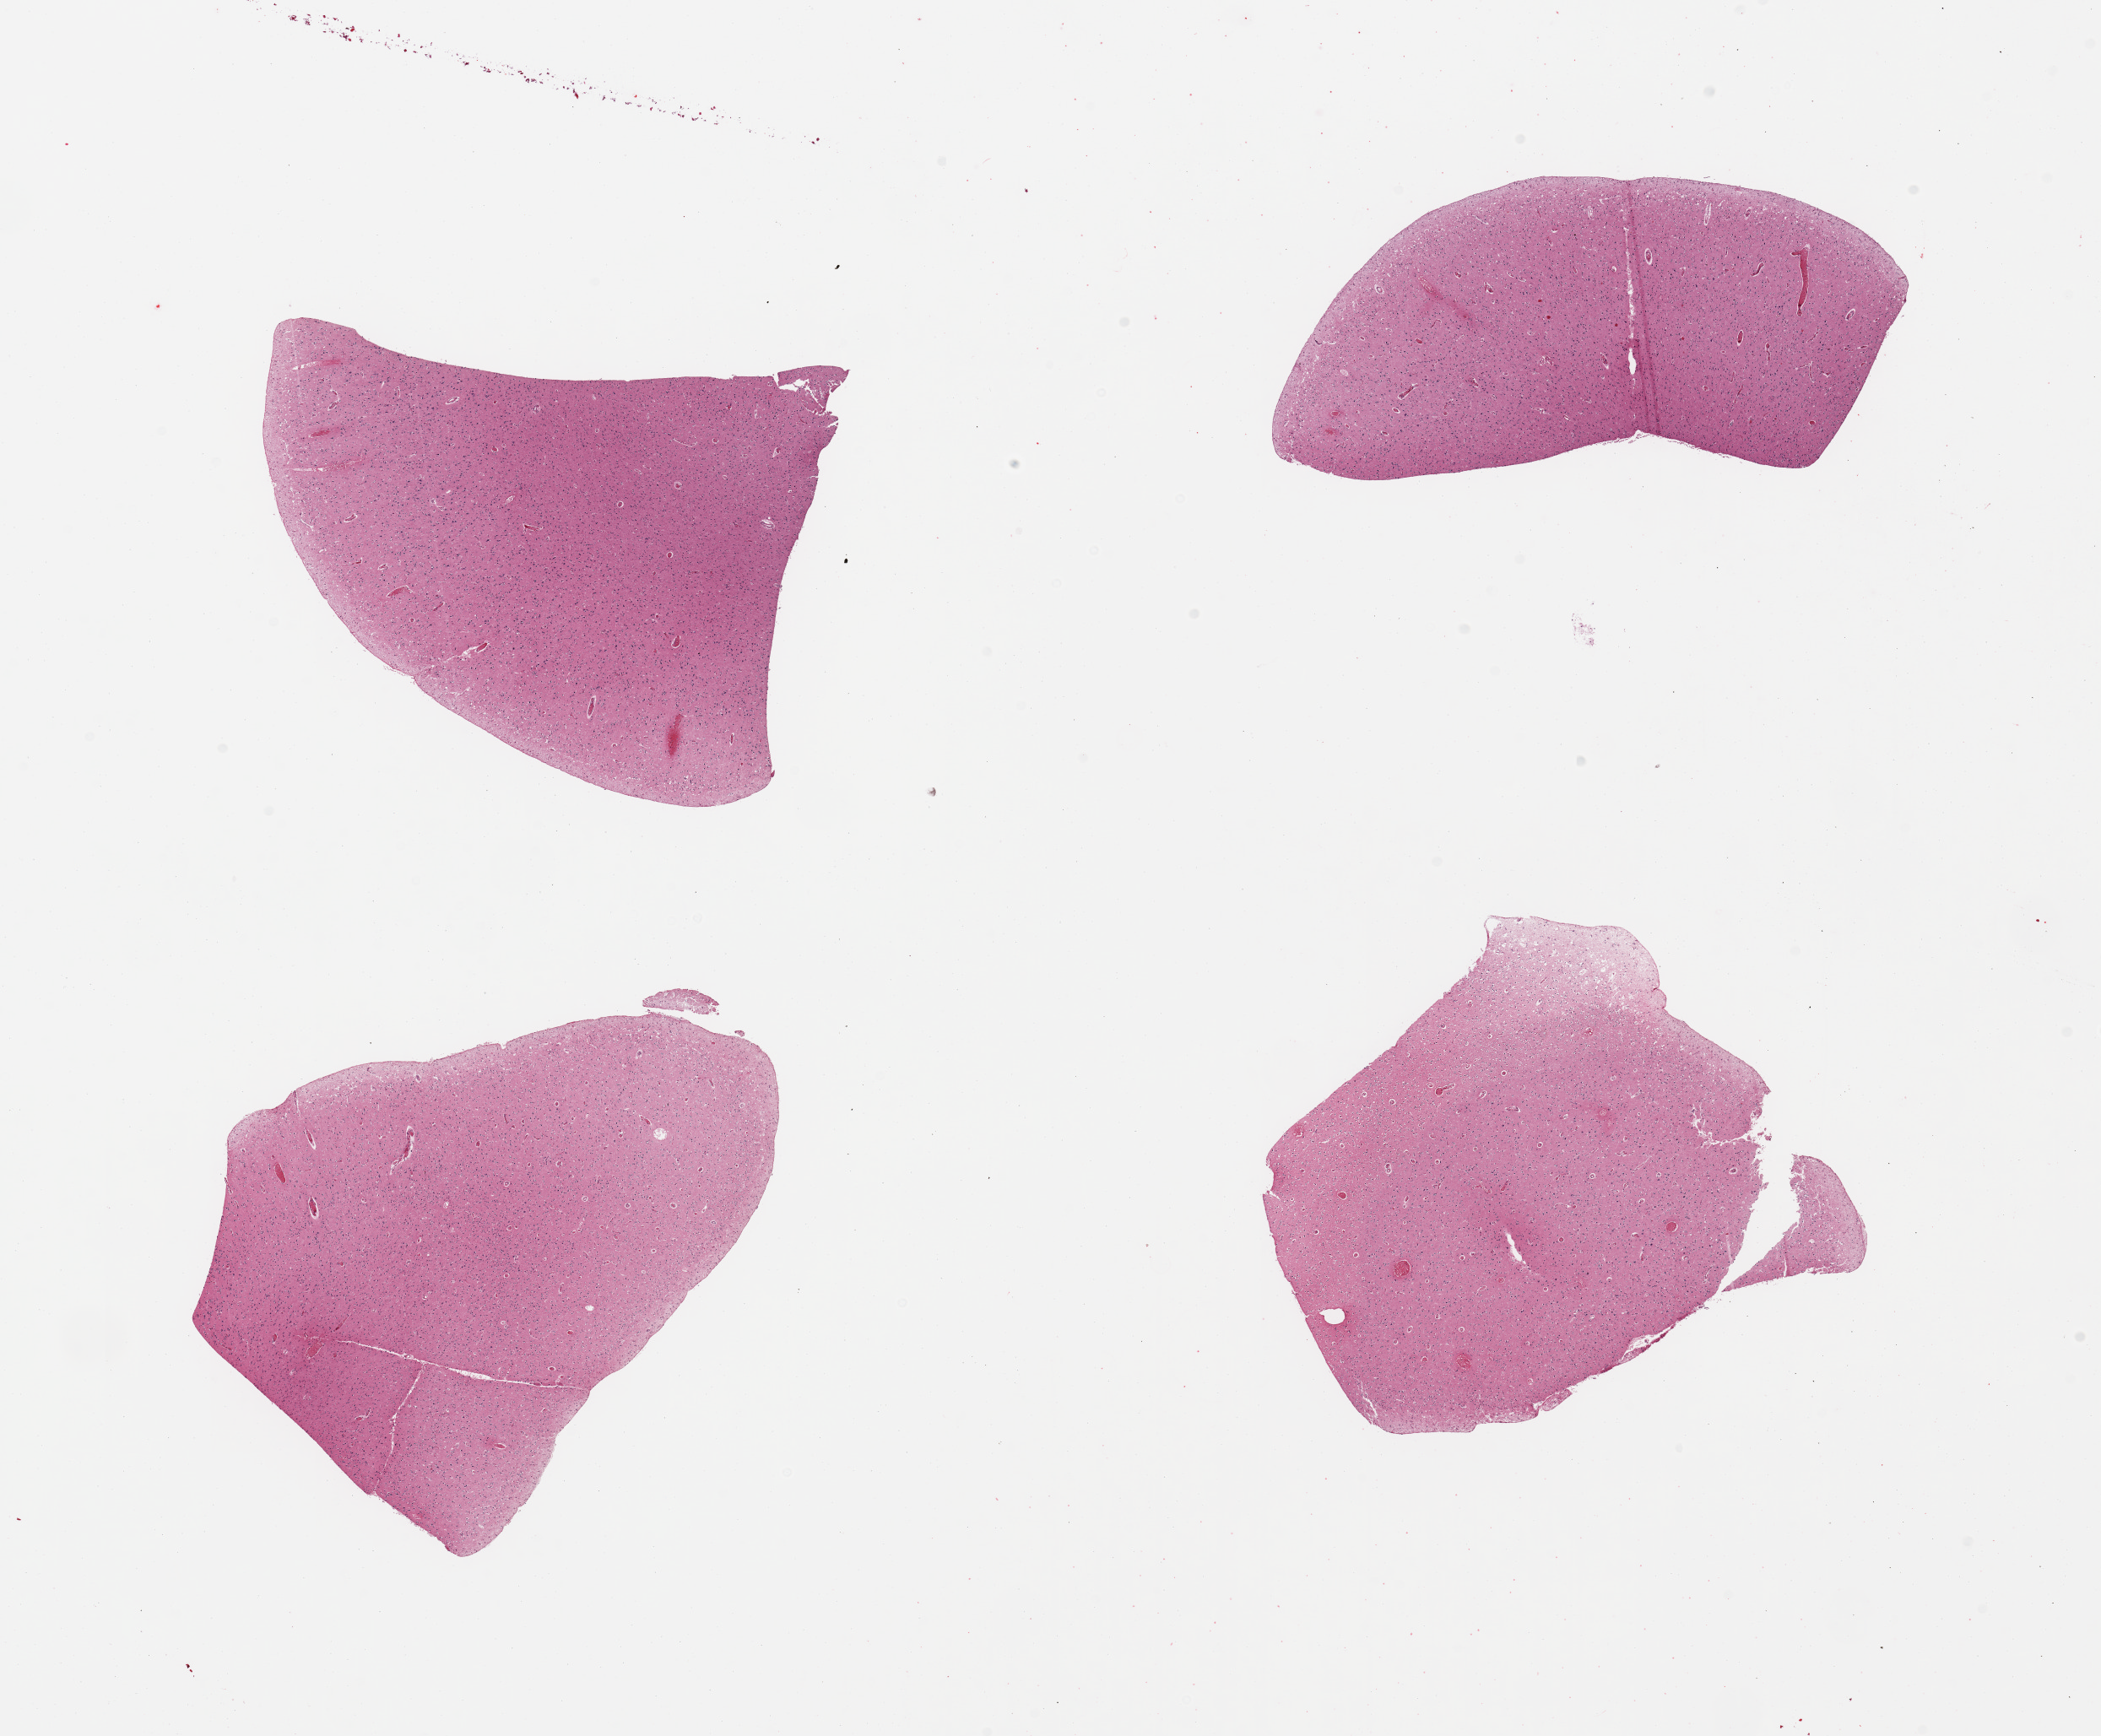
Whole-slide image, hematoxylin and eosin (H&E) stain, whole scanned area (about 19.7 x 16.3 mm, slide scanned at 20x) shown as a low-resolution overview, PAXgene-fixed, paraffin-embedded tissue, section of cerebral cortex (target tissue), donor tissue sample. Donor sex: female.
Pathologist's review note for this sample: 4 pieces.